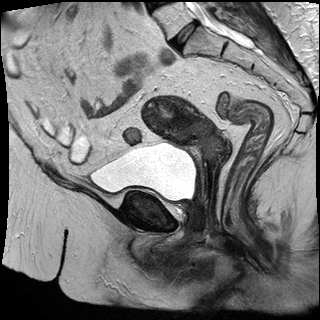
Pelvic MRI for cervical cancer, one sagittal slice. Slice 18 of 32 in the series (ordered by position). T2-weighted. 1.5 T. TE 87 ms, TR 3063.4 ms. 320 × 320 image matrix, field of view 280 × 280 mm. Patient: female, 53 years.
Structures marked on this image (outlined manually by an expert reader):
- uterus and cervix: box from (x=141, y=95) to (x=226, y=164) px